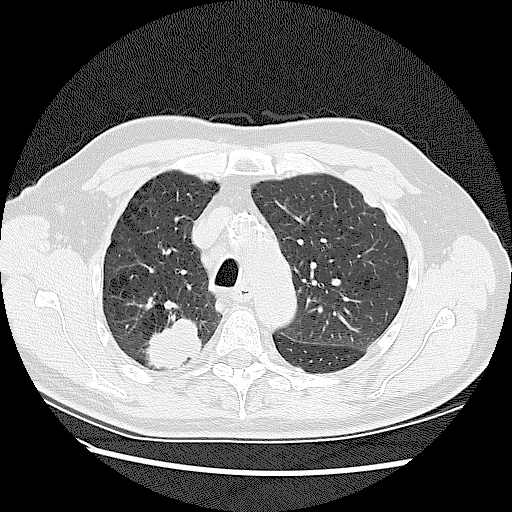
Low-dose screening chest CT, one axial slice. Position 93 of 128 along the scan axis. Reconstruction kernel LUNG. 120 kVp. Lung window (W 1500 / L -600 HU). 512 × 512 image matrix, field of view 360 × 360 mm.
Structures marked on this image (manually delineated by an expert):
- lesion 2 (tumor, upper lobe of right lung): bounding box [x1, y1, x2, y2] px = [147, 317, 202, 368]